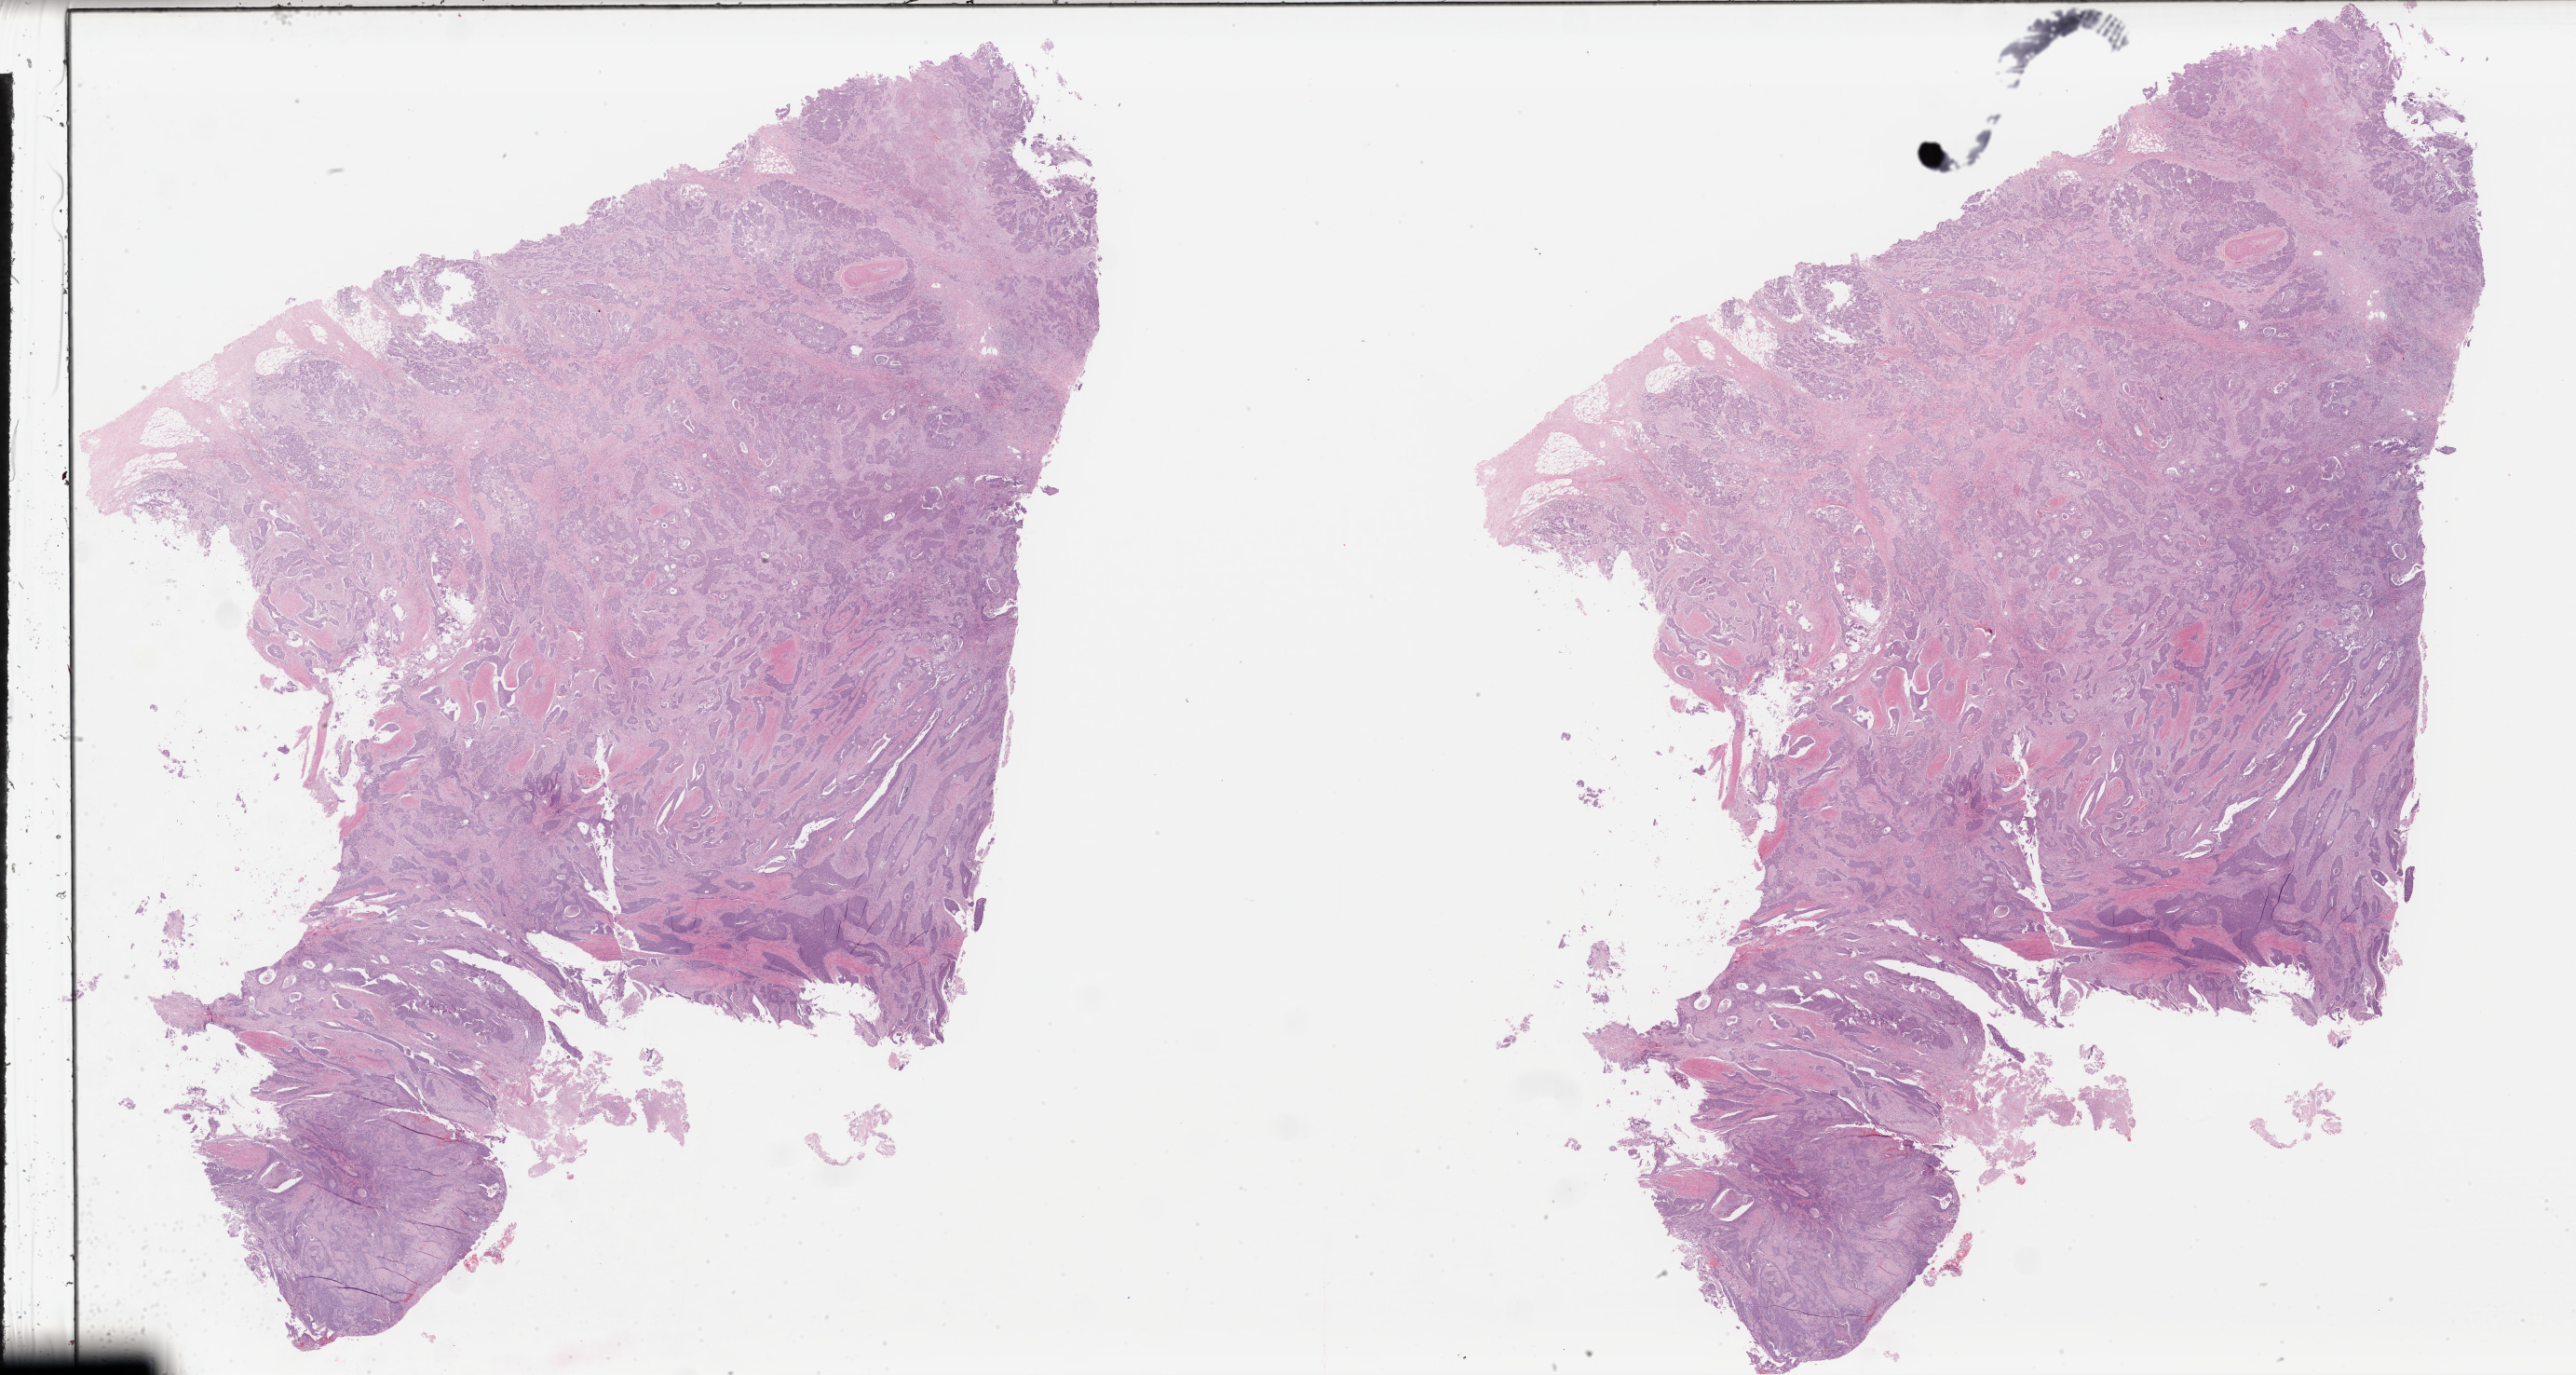
Digitized Hematoxylin and eosin (H&E) stained tissue section (whole slide) — whole scanned area (about 43.7 x 23.3 mm, from a 40x scan) shown as a low-resolution overview; formalin-fixed paraffin-embedded (FFPE) diagnostic section; primary tumour sample from the bladder. Female, age 70 years at initial diagnosis. Histologic grade: high grade.
• TNM: T3a N0 M0
• diagnosis: Transitional cell carcinoma (trigone of bladder)
• AJCC pathologic stage: III (6th edition)